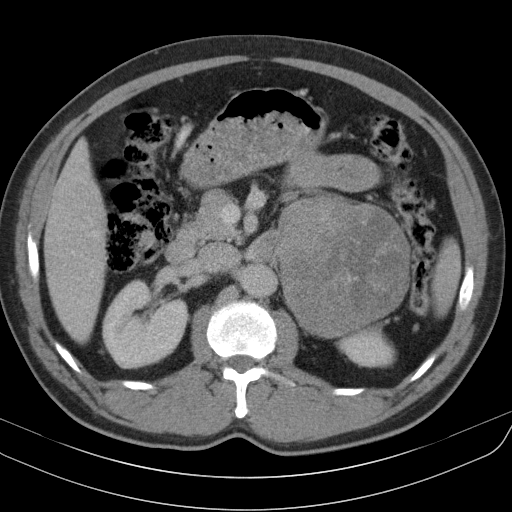
Contrast-enhanced abdominal CT, one axial slice; slice 63 of 91 in the series (ordered by position); intravenous contrast given; soft-tissue window (W 400 / L 40 HU); 512 × 512 image matrix, field of view 370 × 370 mm. Patient: male, 51 years. Case-level facts recorded for this patient, not image findings: diagnosis: adrenocortical carcinoma; tumour side: left adrenal; tumour size at pathology: 18 cm; Ki-67 index: 40 %.
Outlined on this slice (semi-automatic segmentation, software-assisted and operator-edited):
- mass: box from (x=279, y=197) to (x=407, y=334) px